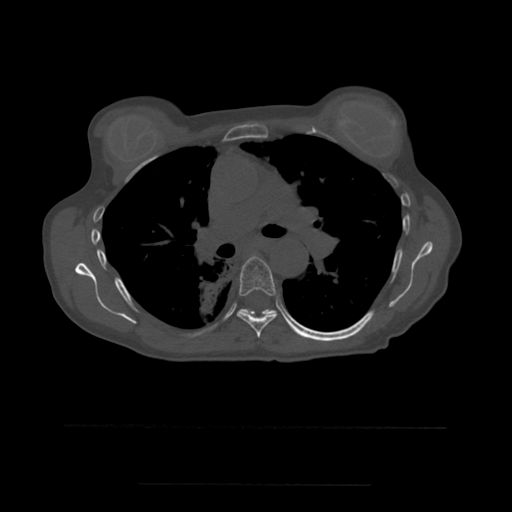
CT including the spine, one axial slice. Slice 373 of 544 in the series (ordered by position). Bone window (W 1800 / L 400 HU). 512 × 512 image matrix, field of view 350 × 350 mm. Patient age 58 years. From the clinical record (not read from this slice): primary cancer: lung.
Structures marked on this image (semi-automatic segmentation, software-assisted and operator-edited):
- T6 vertebra: bounding box (x1, y1, x2, y2) in pixels: (237, 256, 278, 338)
- T7 vertebra: (242, 309, 274, 314)